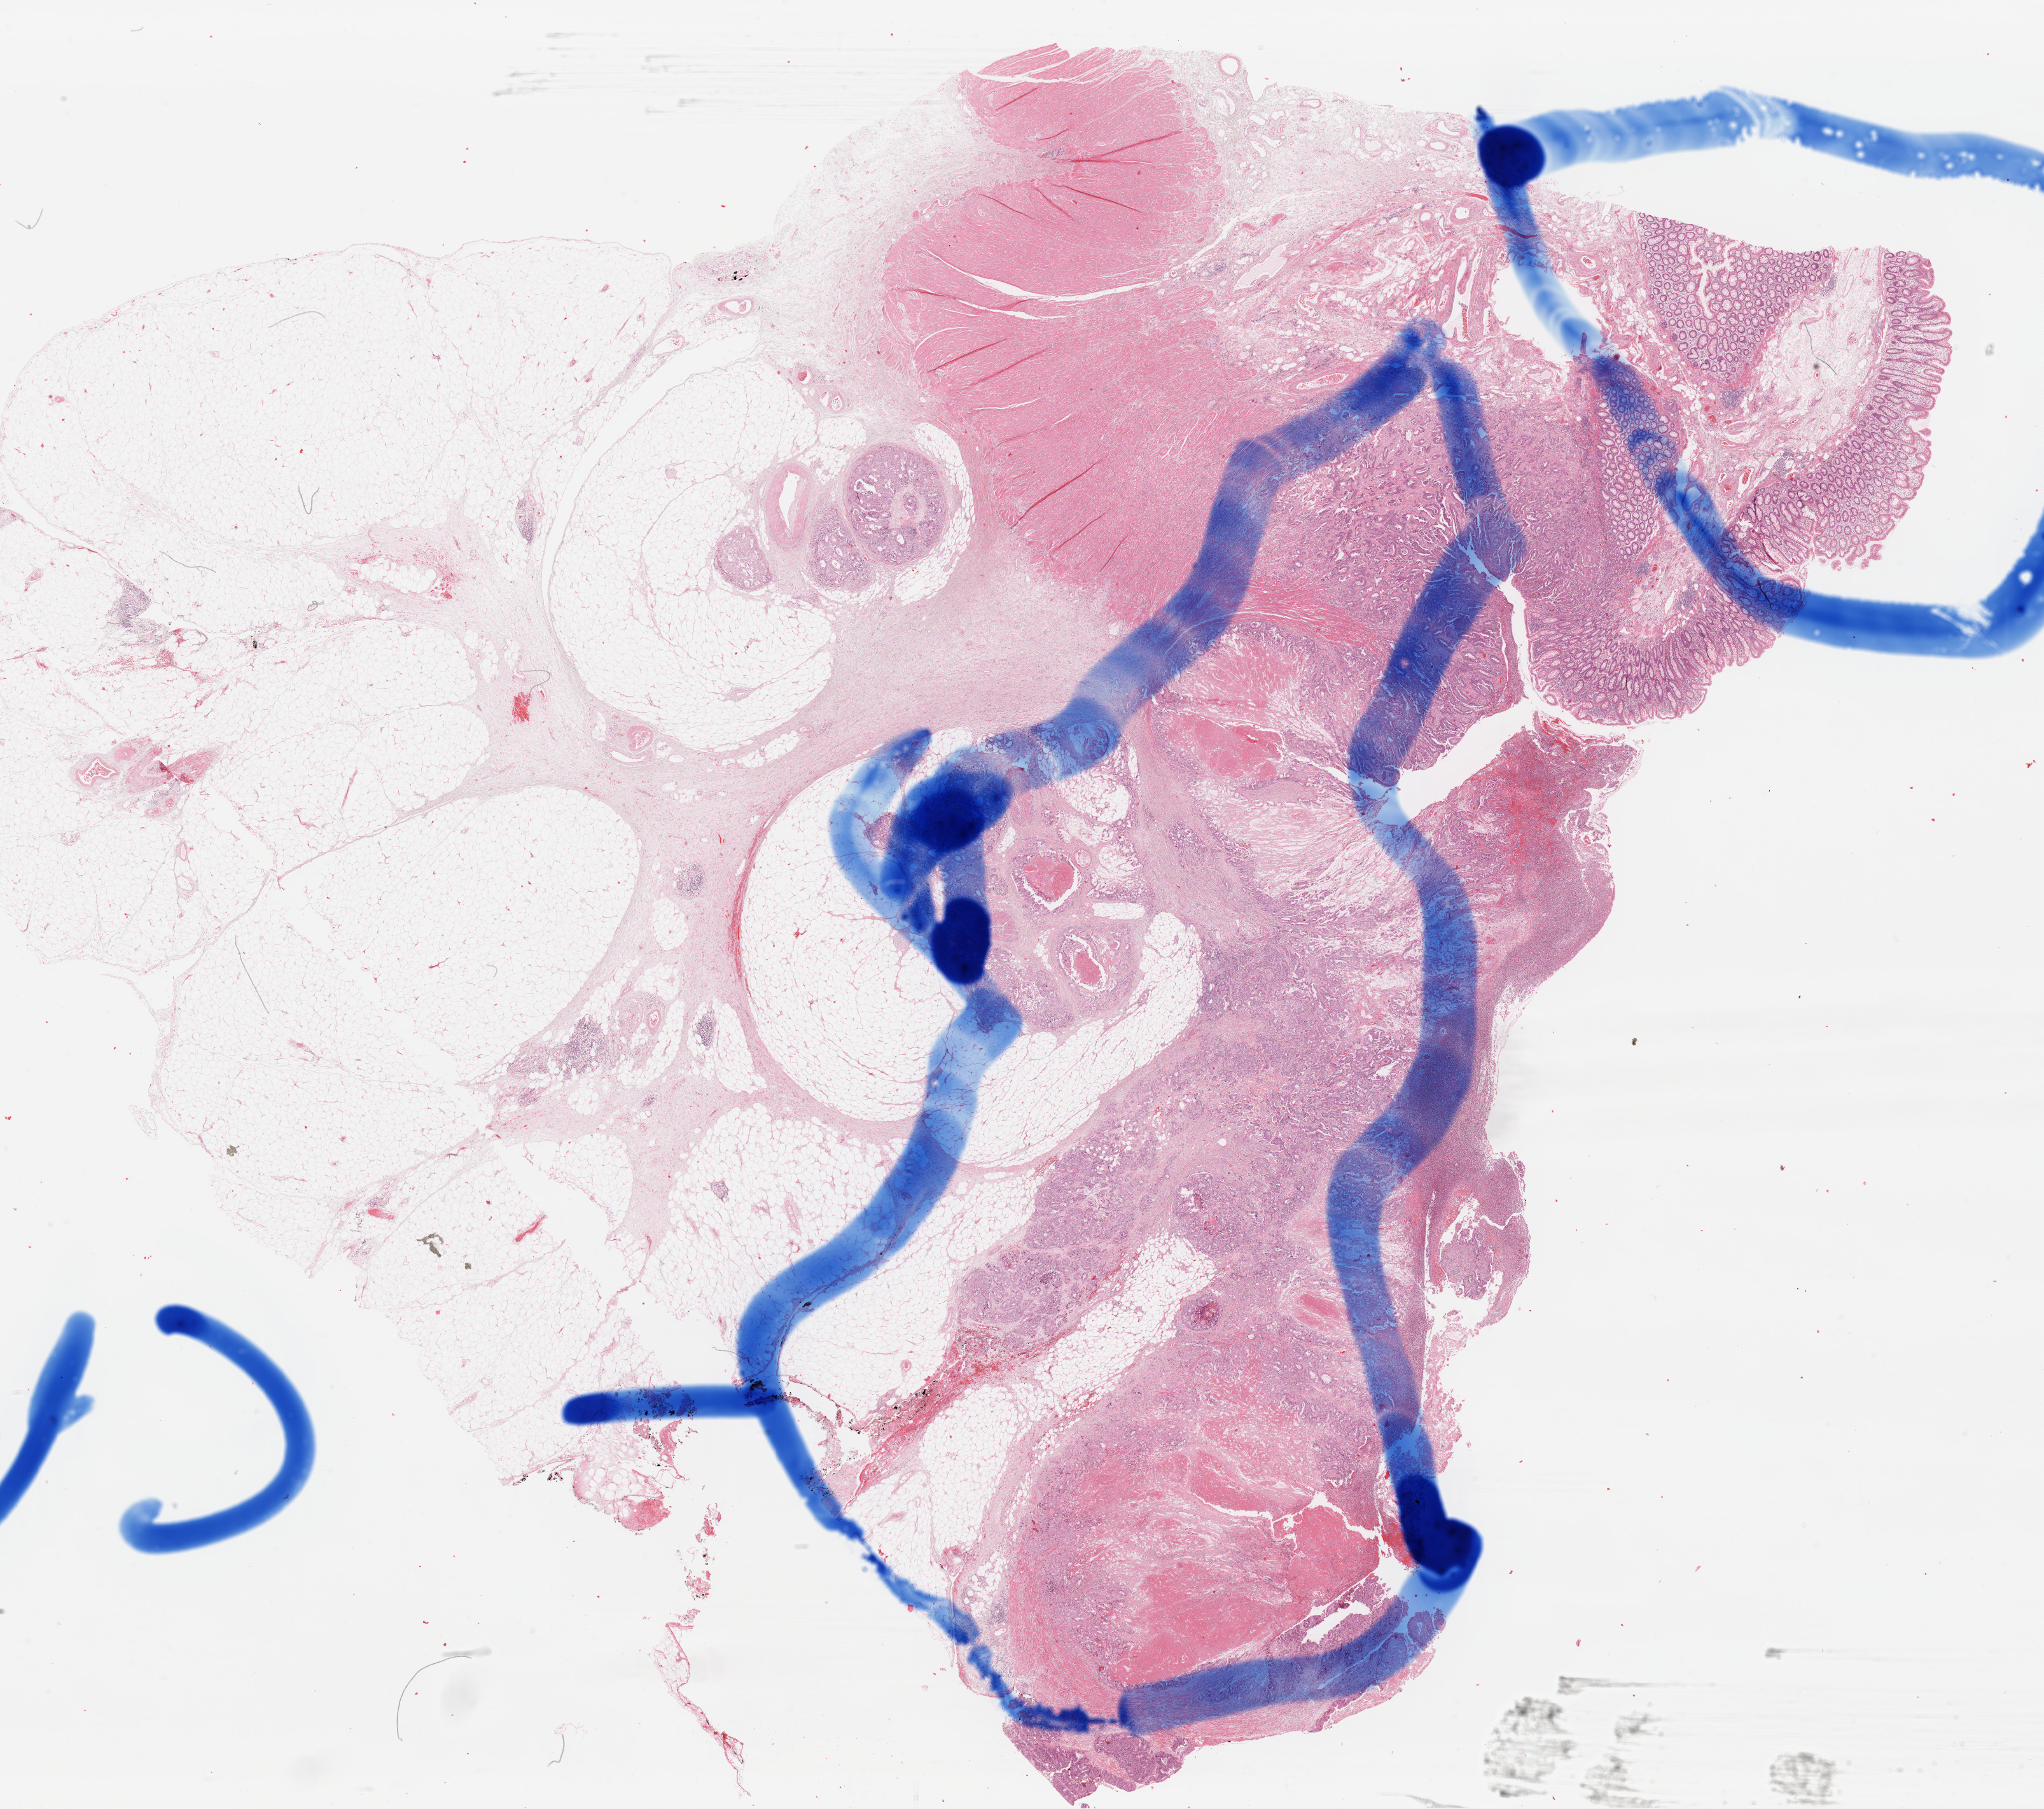
Whole-slide histology image, H&E-stained, shown as a low-resolution overview of the whole scanned area (about 25.4 x 22.5 mm, from a 40x scan). FFPE section. Primary tumour sample from the colon. Female, age 71 years at initial diagnosis.
• diagnosis: Mucinous adenocarcinoma (ascending colon)
• AJCC pathologic stage: IV